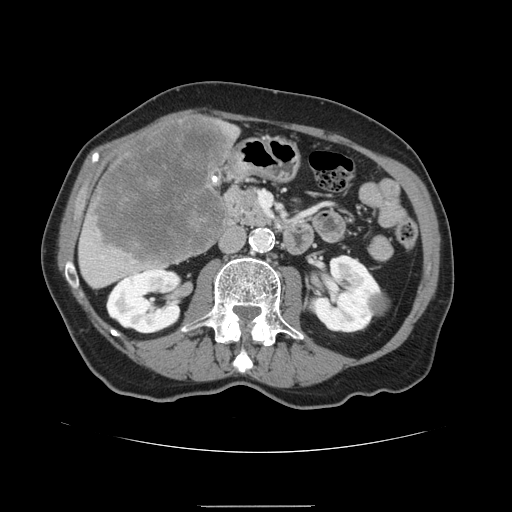
Contrast-enhanced abdominal CT, one axial slice. Position 55 of 168 along the scan axis. Soft-tissue window (W 400 / L 40 HU). 512 × 512 image matrix, field of view 386 × 386 mm. Male patient, age 74 years. Case-level facts recorded for this patient, not image findings: diagnosis: colorectal cancer liver metastases, imaged before liver resection.
Structures marked on this image (outlined manually by an expert reader):
- liver: bounding box [x1, y1, x2, y2] px = [78, 114, 240, 289]
- liver metastasis: [89, 117, 230, 266]